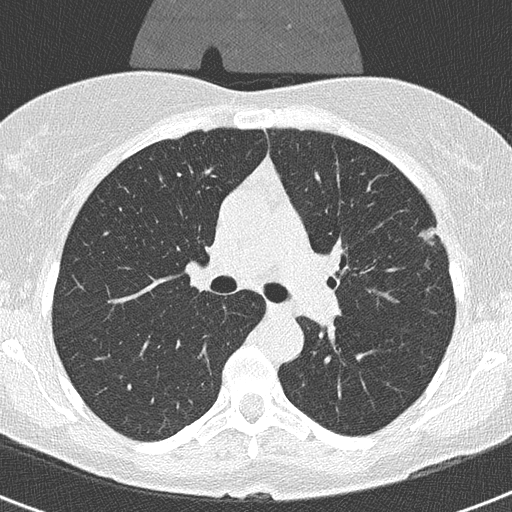
Low-dose screening chest CT, one axial slice. Position 212 of 320 along the scan axis. Reconstruction kernel B50f. 120 kVp. Lung window (W 1500 / L -600 HU). 2 mm slice thickness. 512 × 512 image matrix, field of view 290 × 290 mm.
Outlined on this slice (manually delineated by an expert):
- lesion 1 (tumor, upper lobe of left lung): bounding box (x1, y1, x2, y2) in pixels: (419, 227, 435, 241)